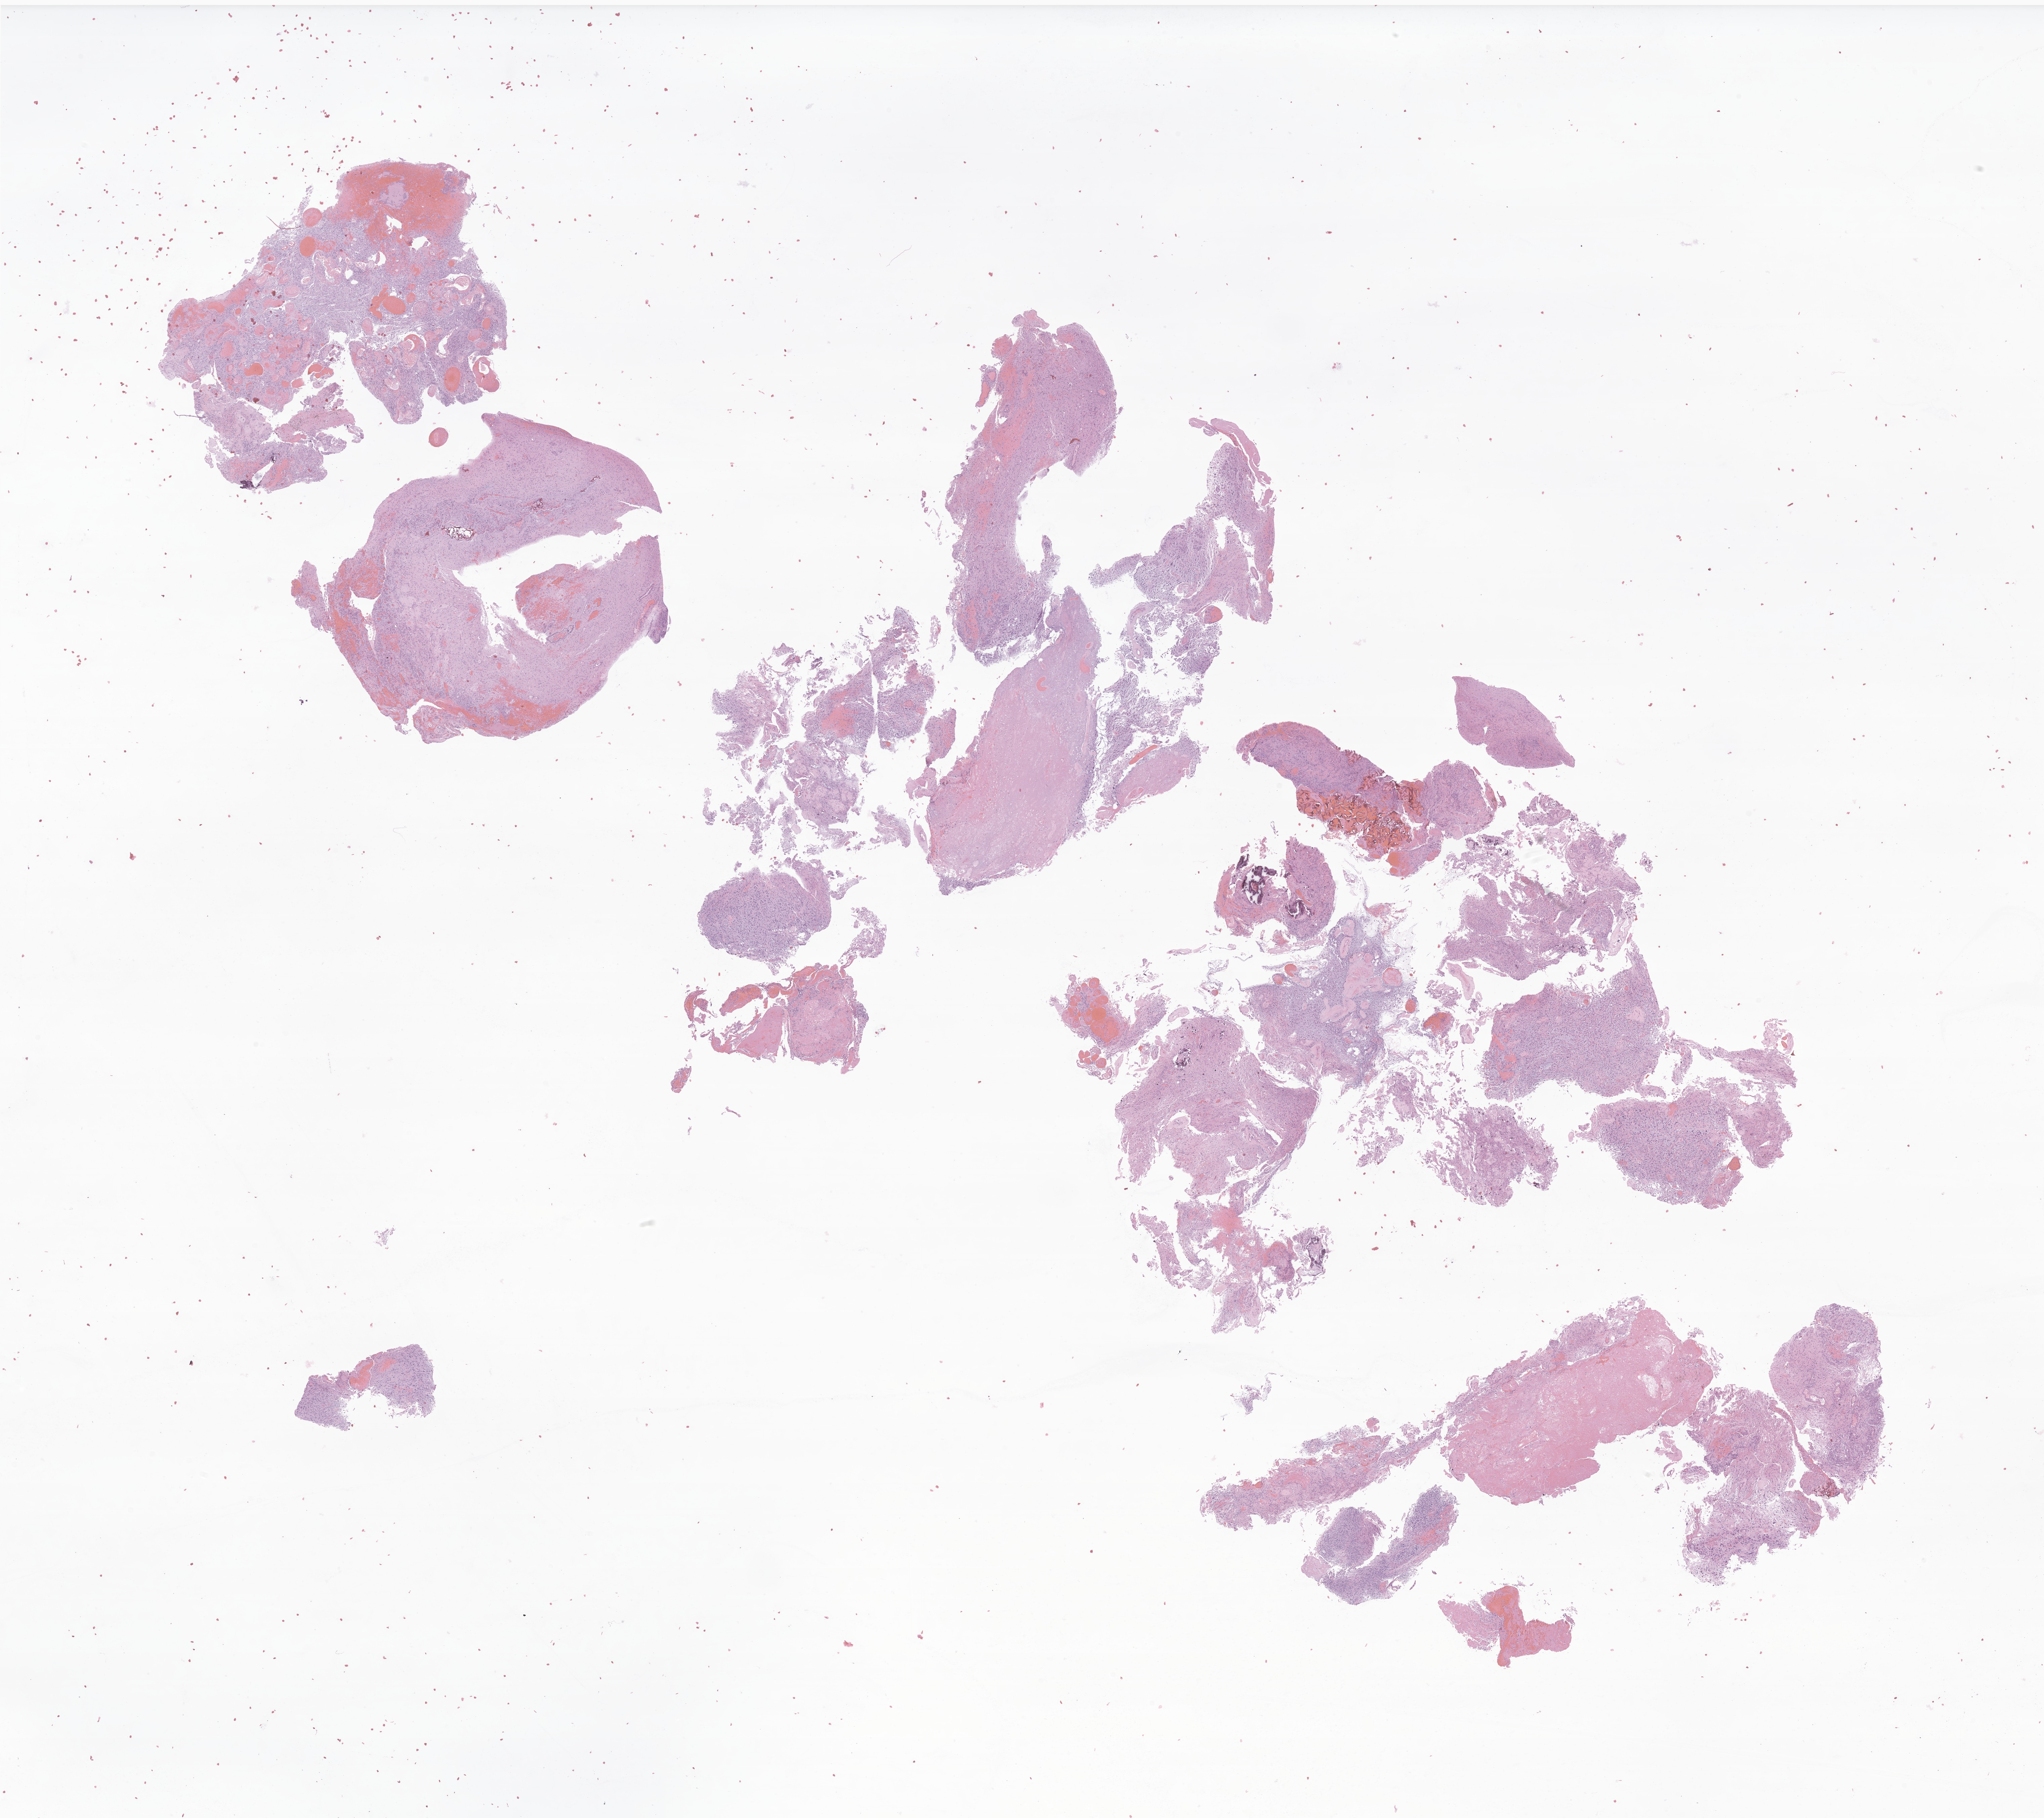
Digitized hematoxylin and eosin (H&E)-stained section of tumor tissue from the spinal cord — a low-resolution overview of the entire scanned area, about 25.6 x 22.8 mm, FFPE section. Male patient, age 216 months.
Diagnosis (ICD-O-3 morphology term): Glioma, malignant.